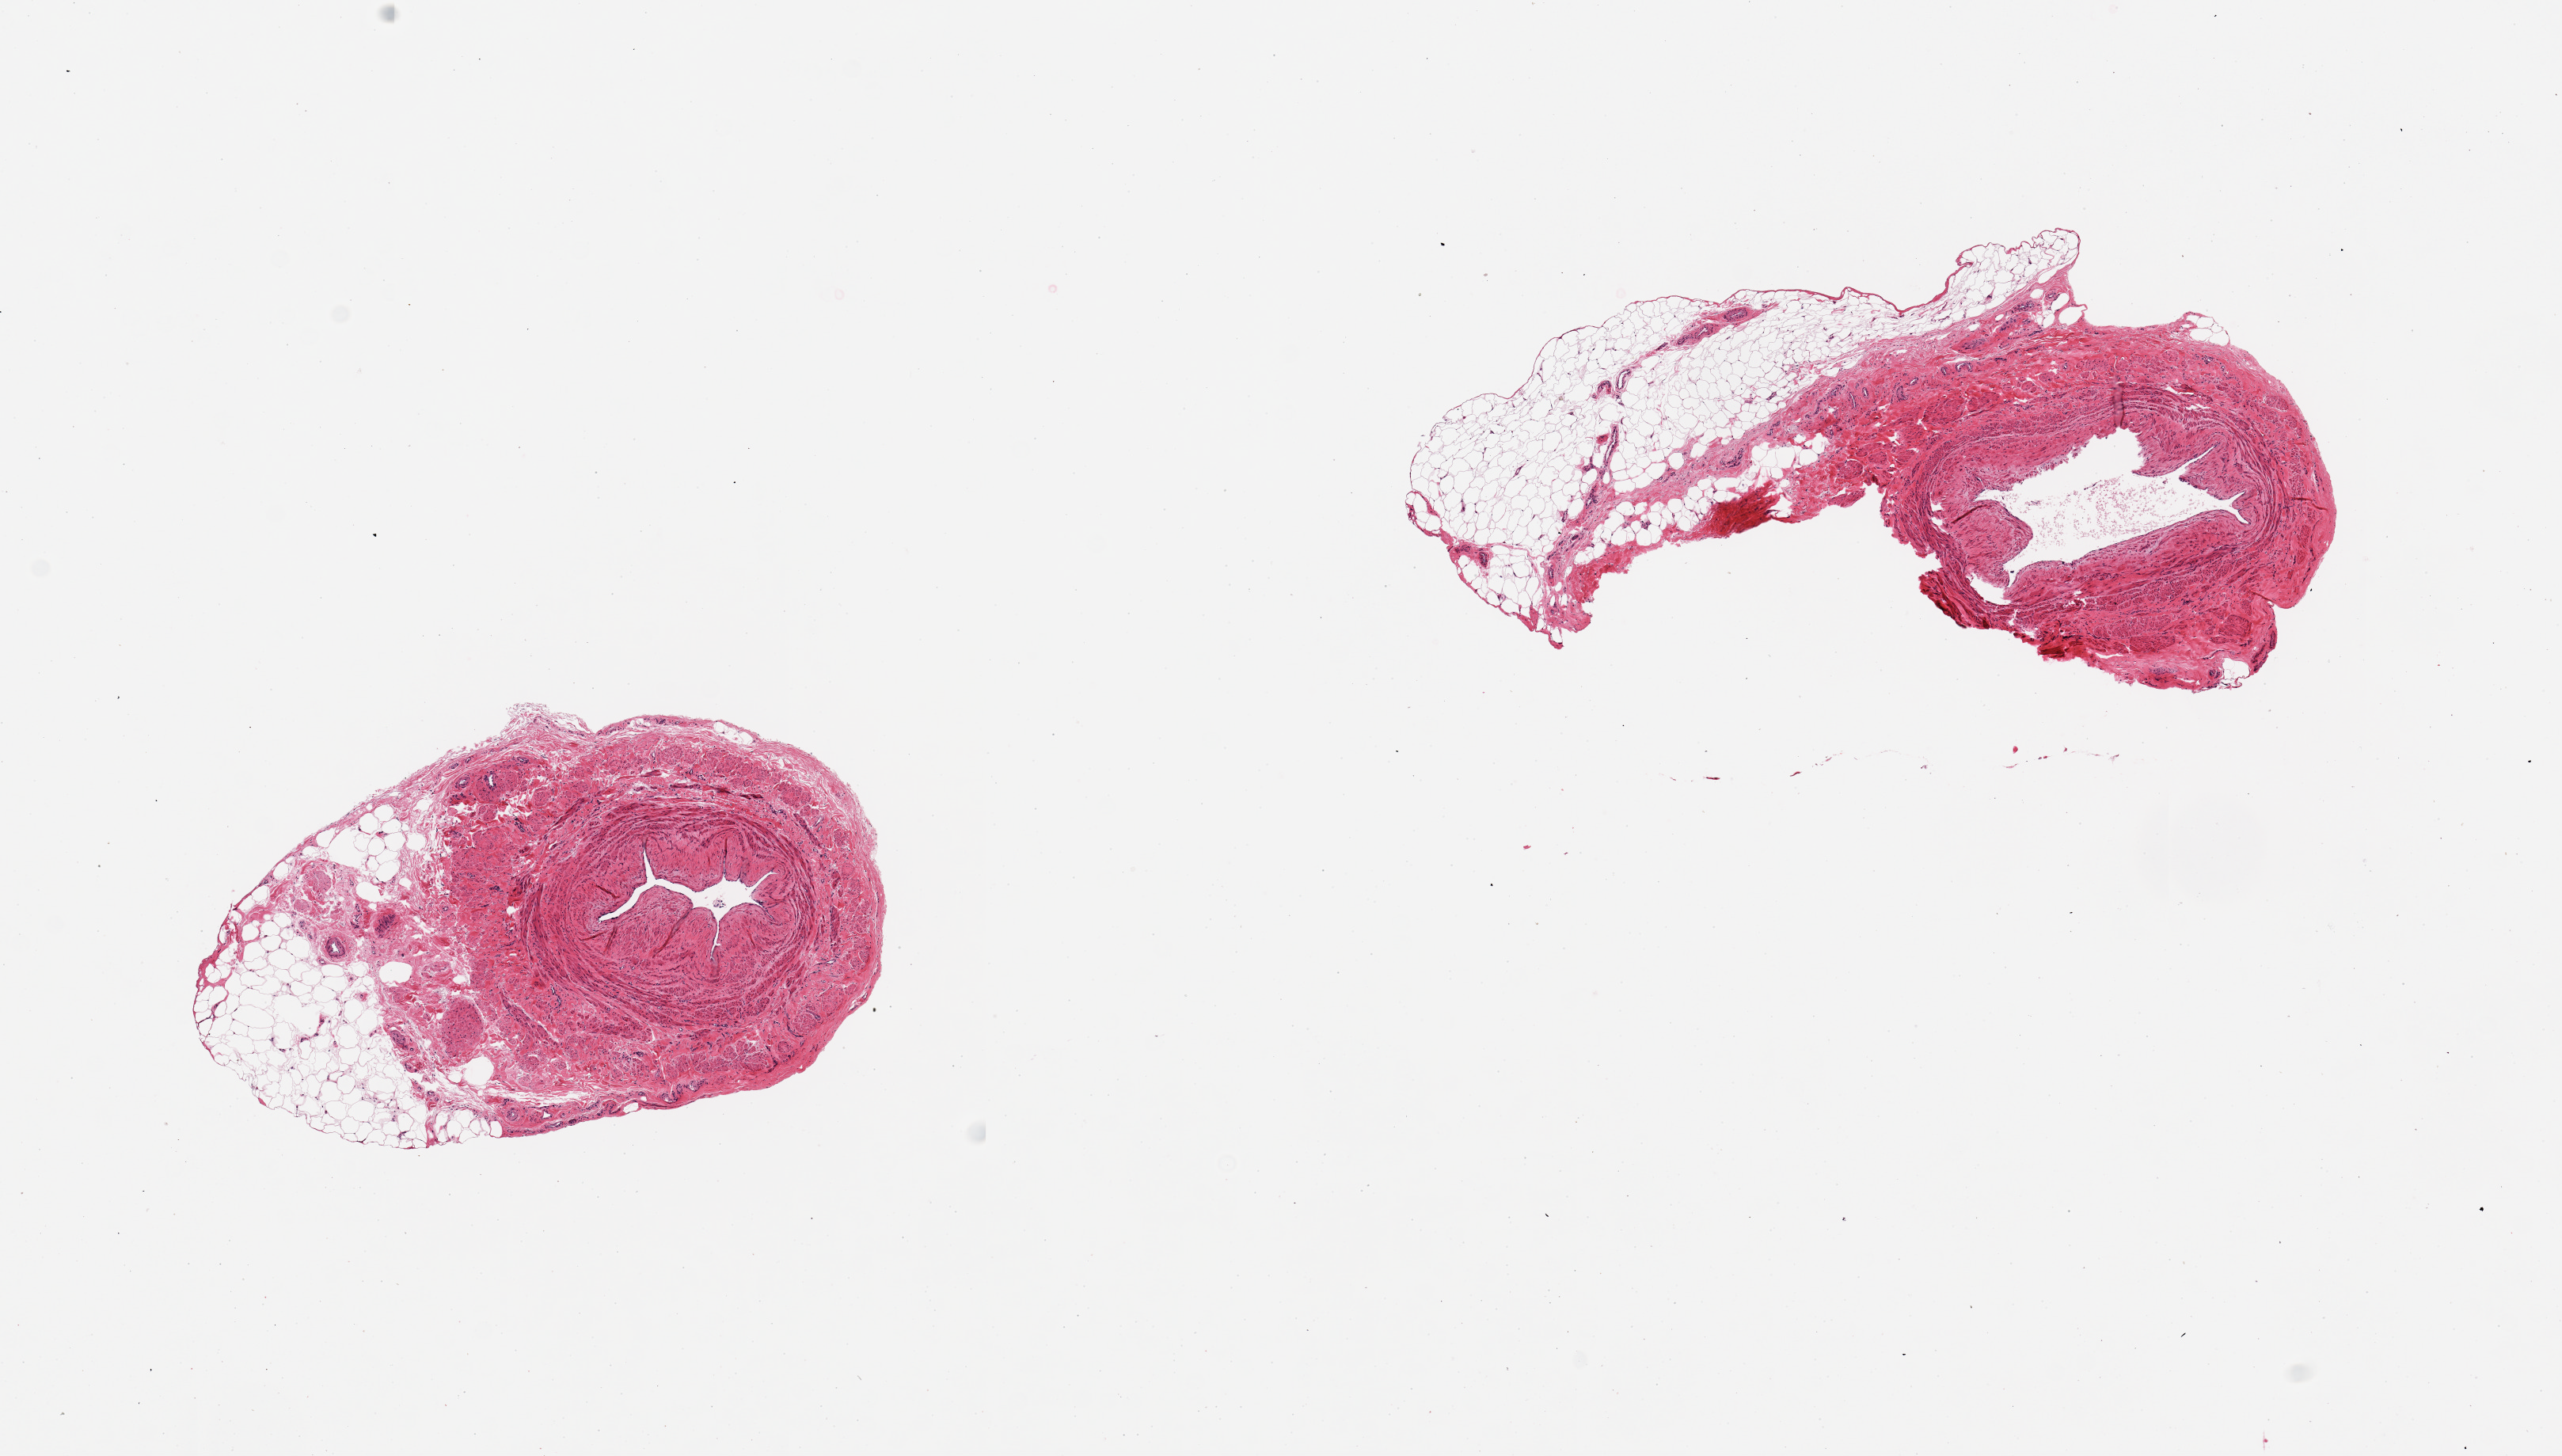
Digitized H&E-stained section, low-resolution overview of the scanned area, about 12.8 x 7.3 mm (slide scanned at 20x), PAXgene-fixed, paraffin-embedded tissue, section of tibial artery (target tissue), tissue donor sample. Donor: female.
Review note (as recorded): 2 pieces adherent fat/fibrous tissue up to ~2mm.